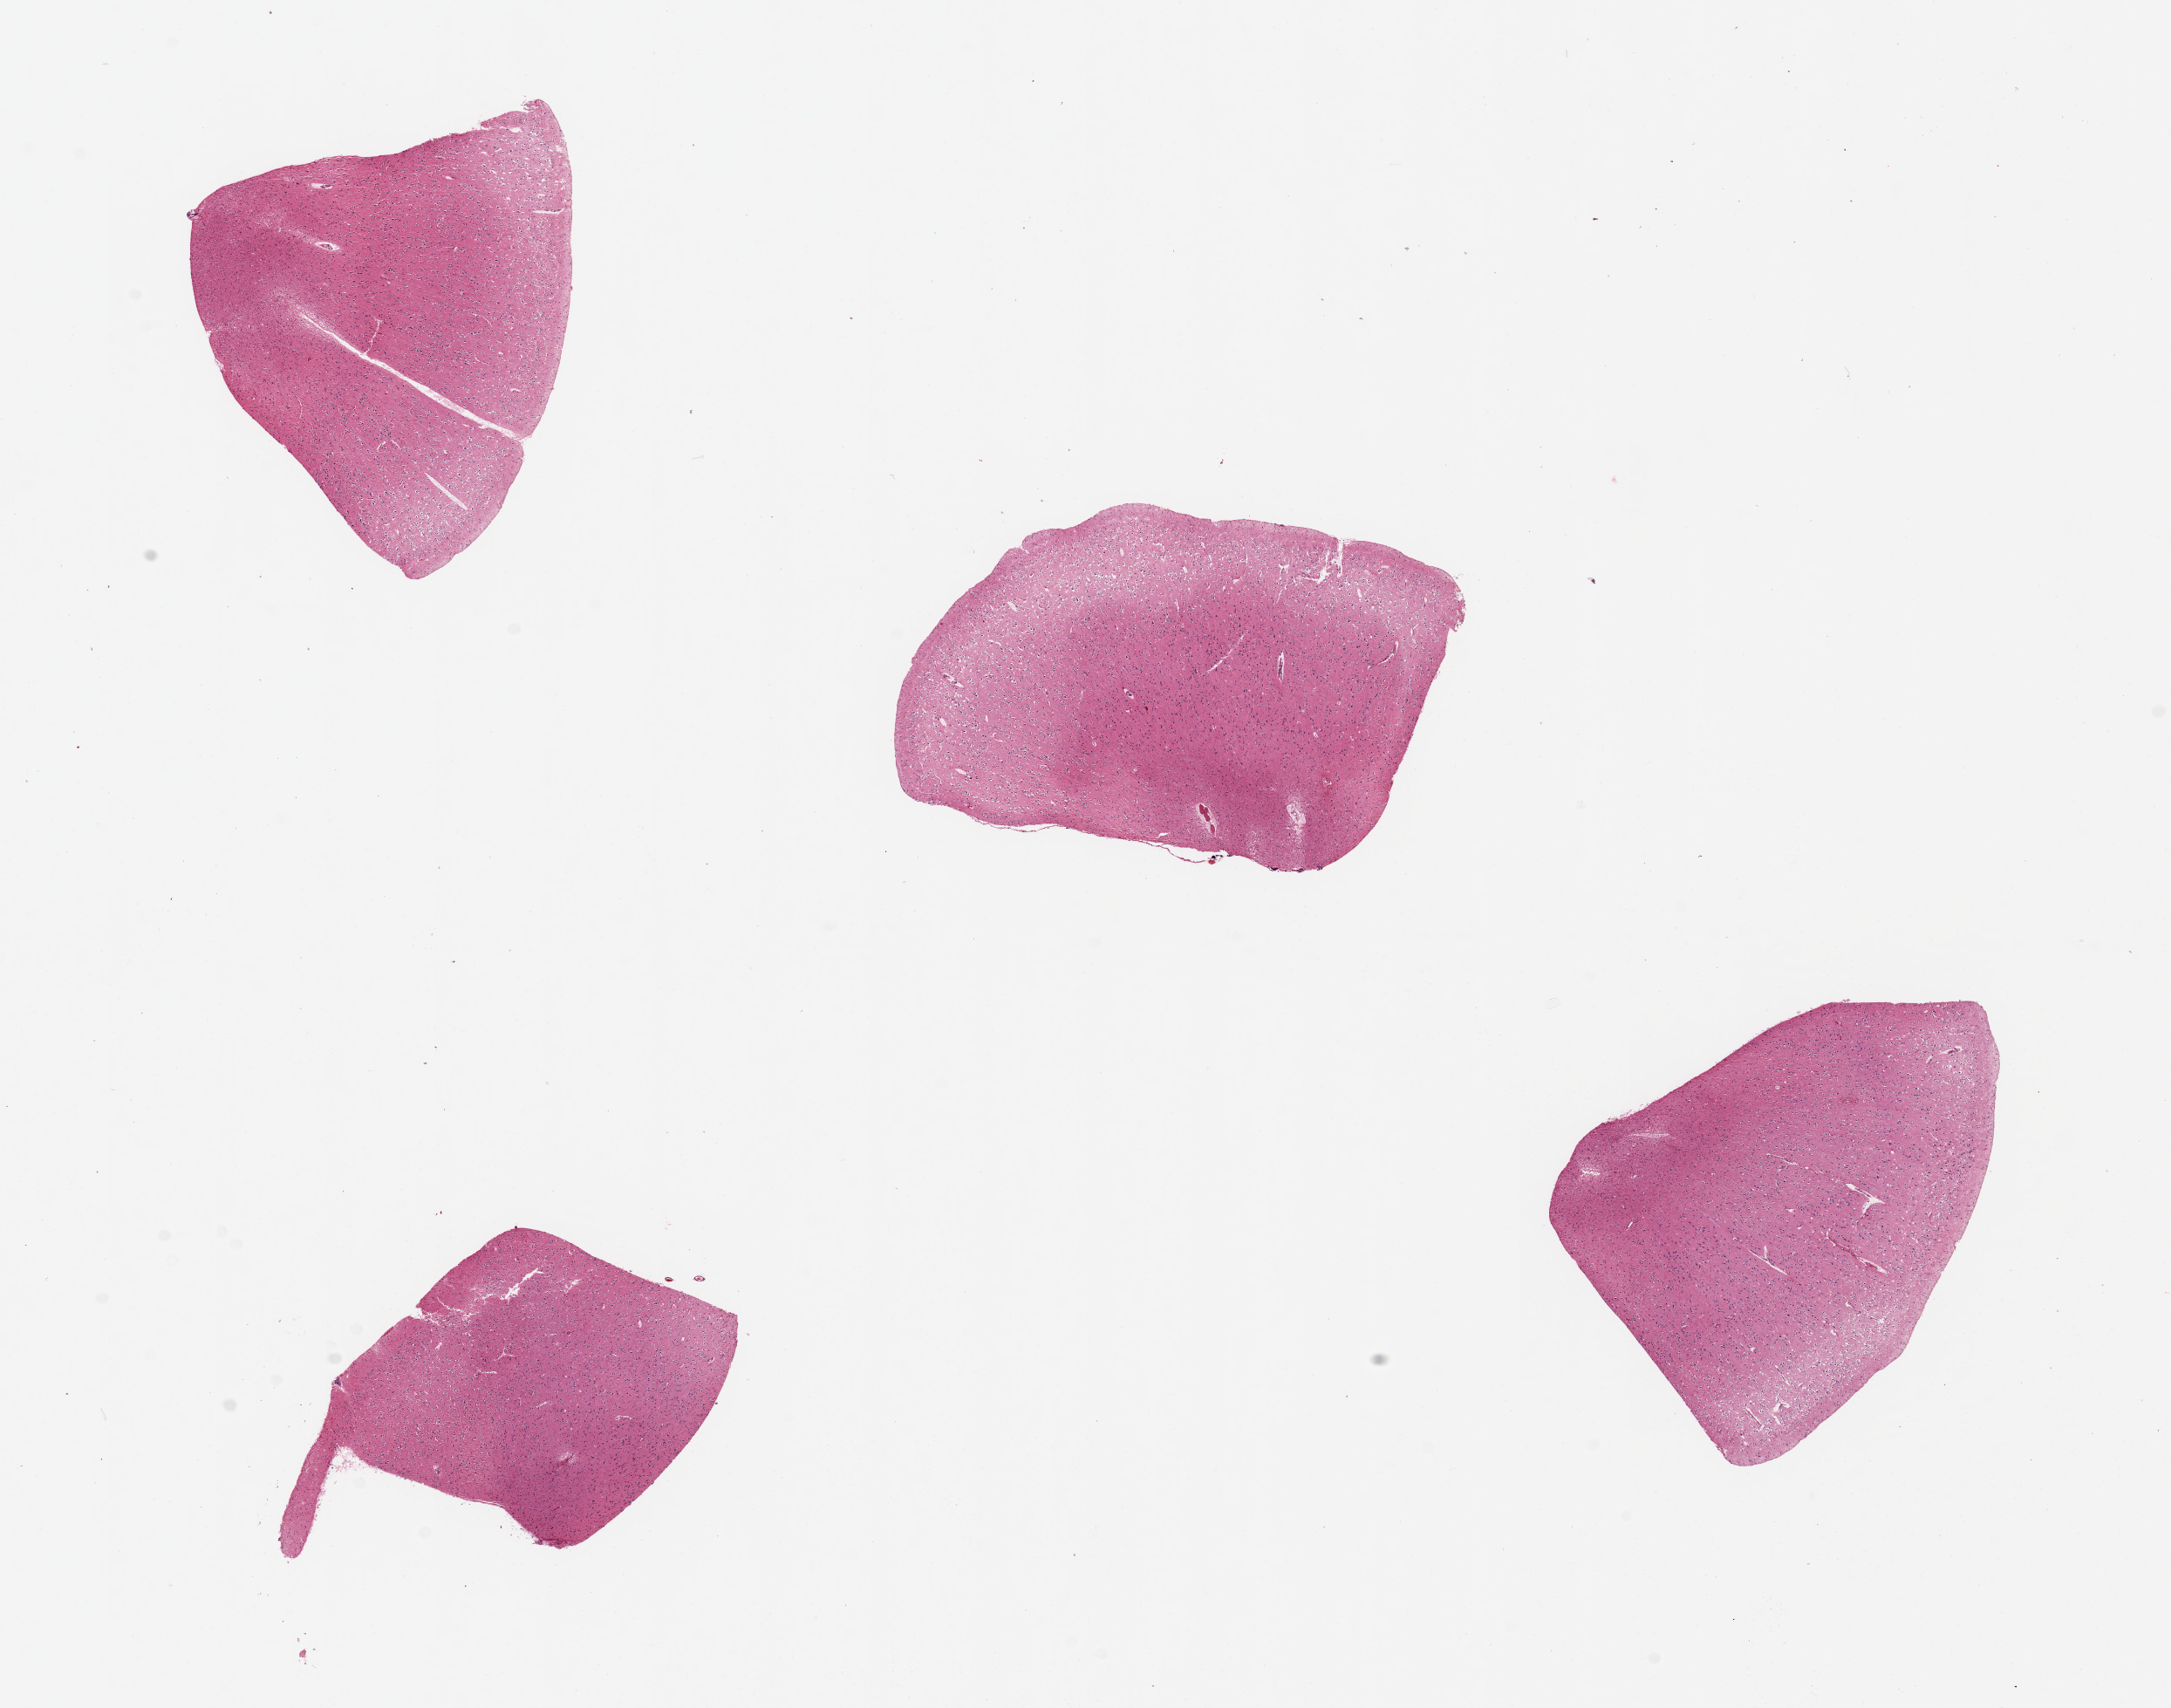
Haematoxylin and eosin whole-slide image, a low-resolution overview of the entire scanned area, about 19.7 x 15.5 mm. PAXgene-fixed paraffin-embedded (PFPE) section. Section of cerebral cortex (target tissue). Donor tissue sample. Donor sex: female.
- reviewer comment on this tissue sample: 4 pieces, up to 4.5x3mm